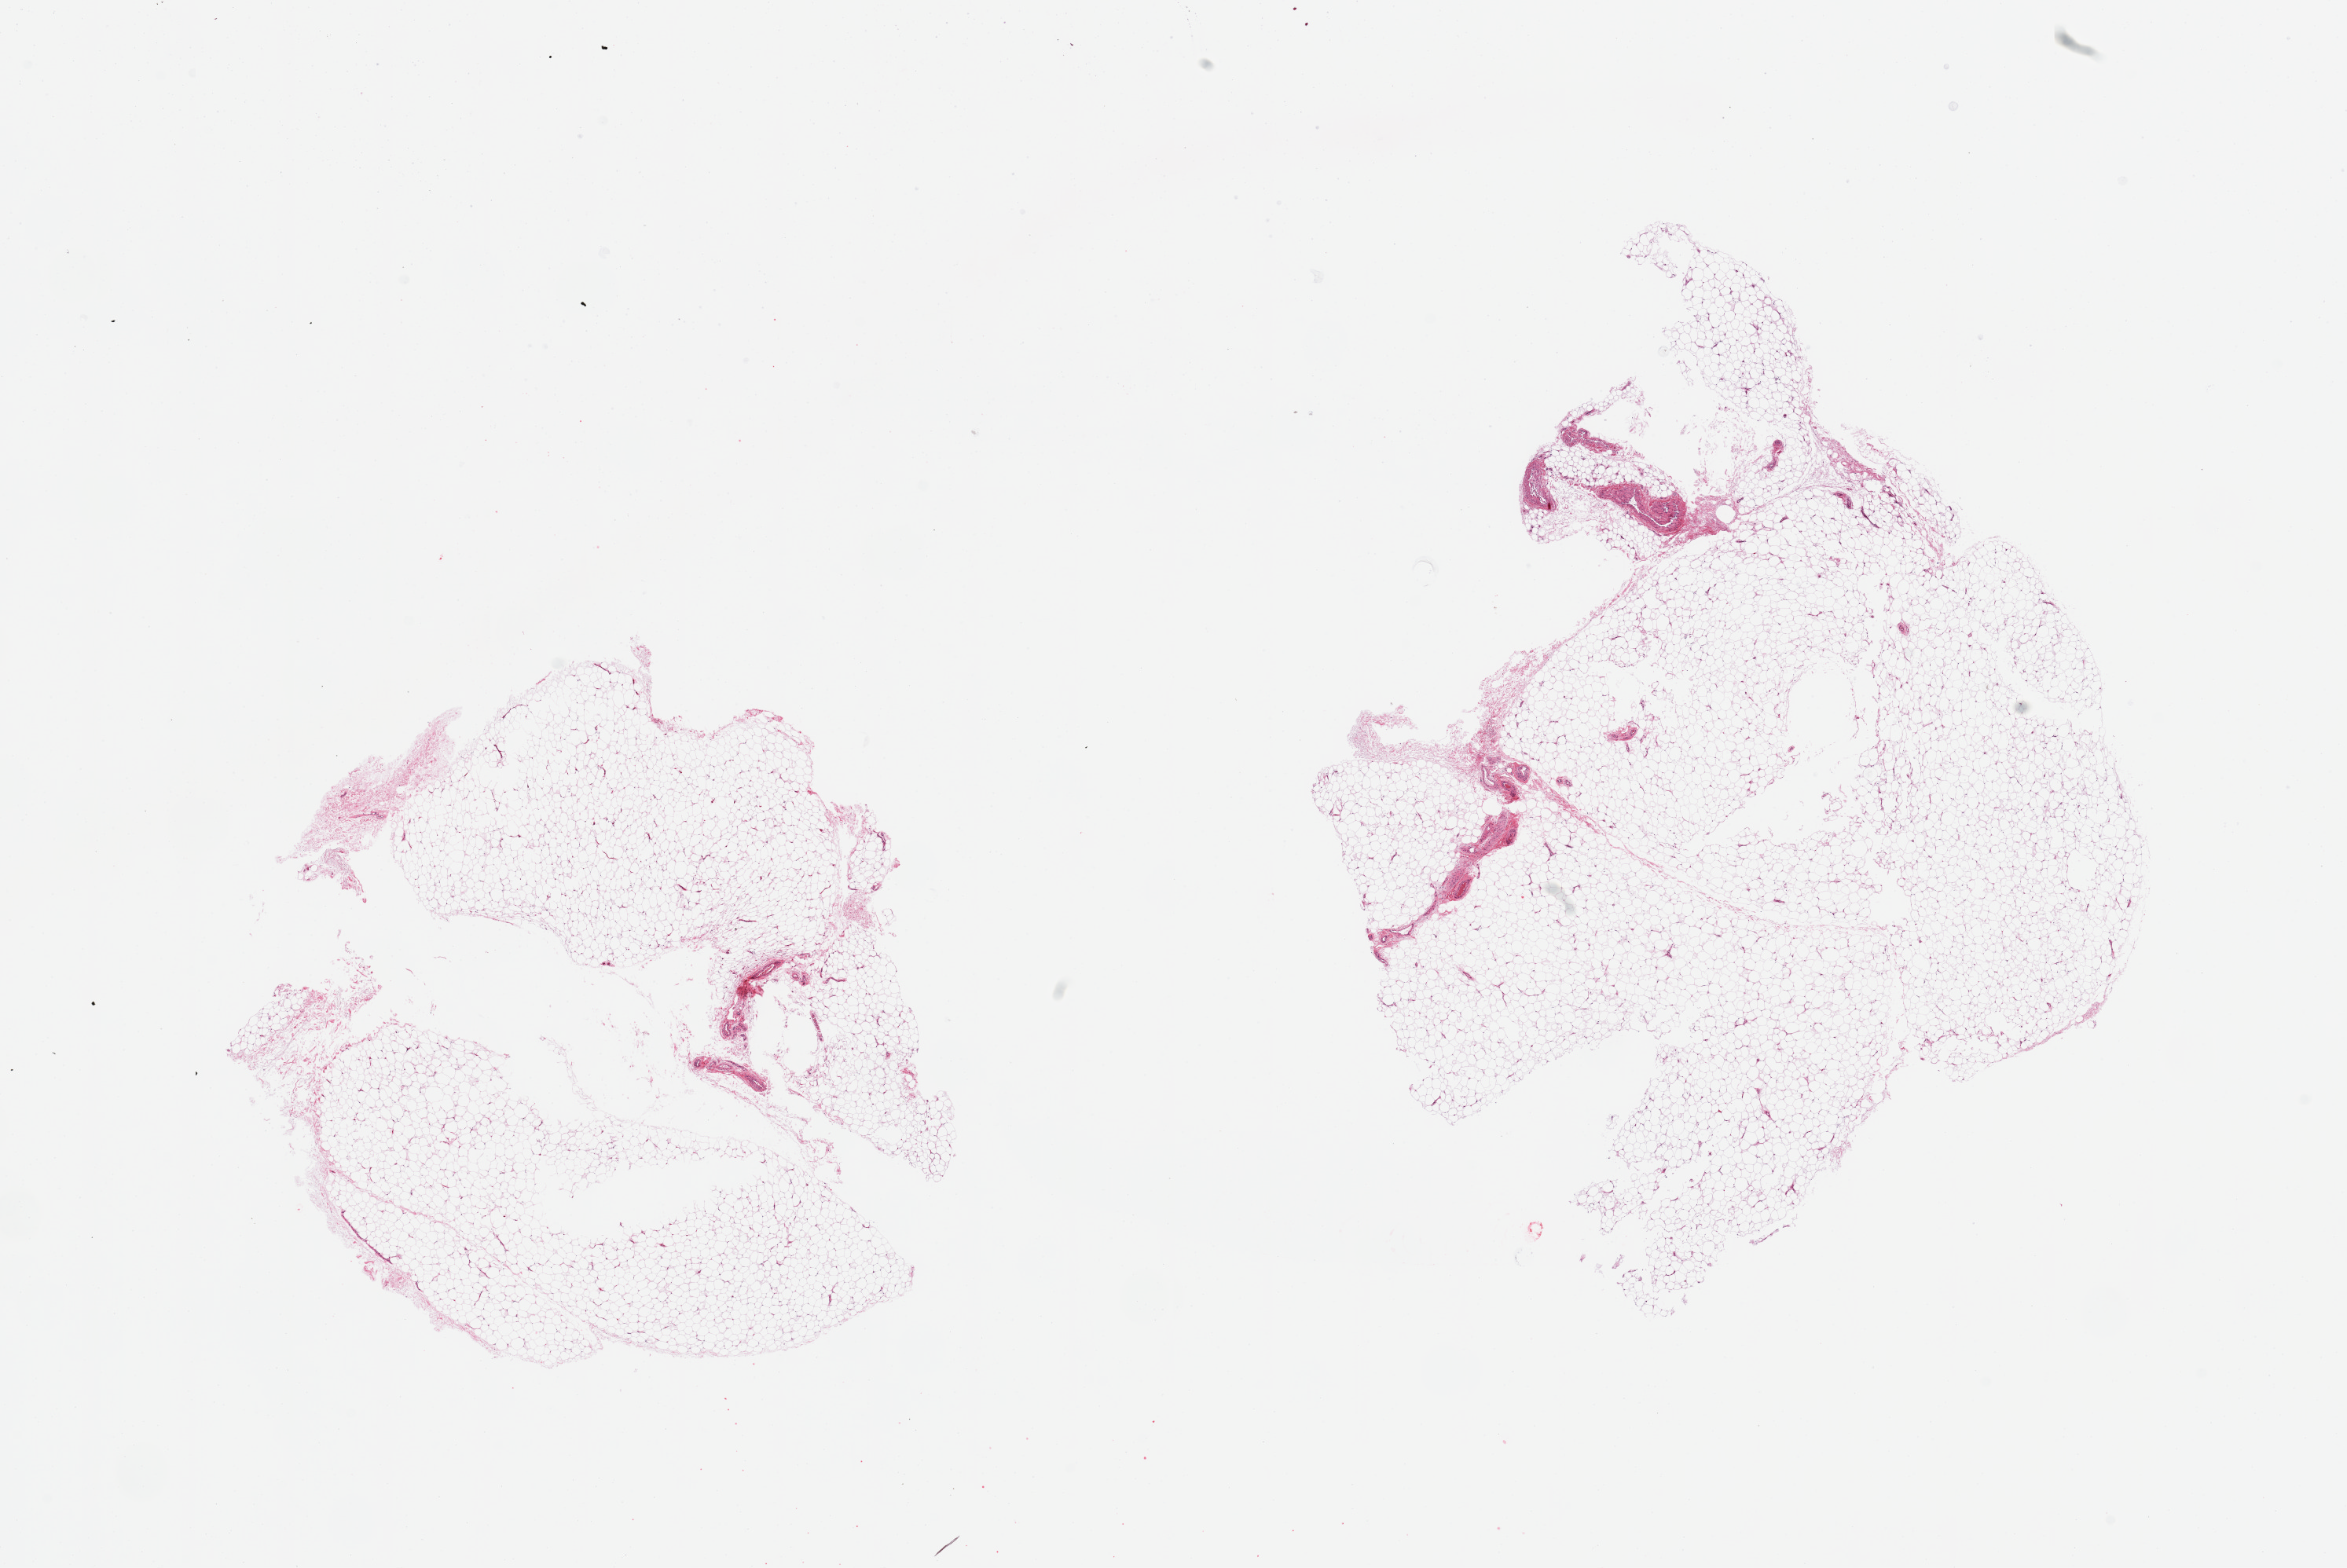
Haematoxylin and eosin whole-slide image, a low-resolution overview of the entire scanned area, about 23.6 x 15.8 mm, PAXgene-fixed paraffin-embedded (PFPE) section, target tissue: adipose tissue, donor tissue sample.
Pathologist's review note for this sample: 2 pieces; minimal fibrous content.